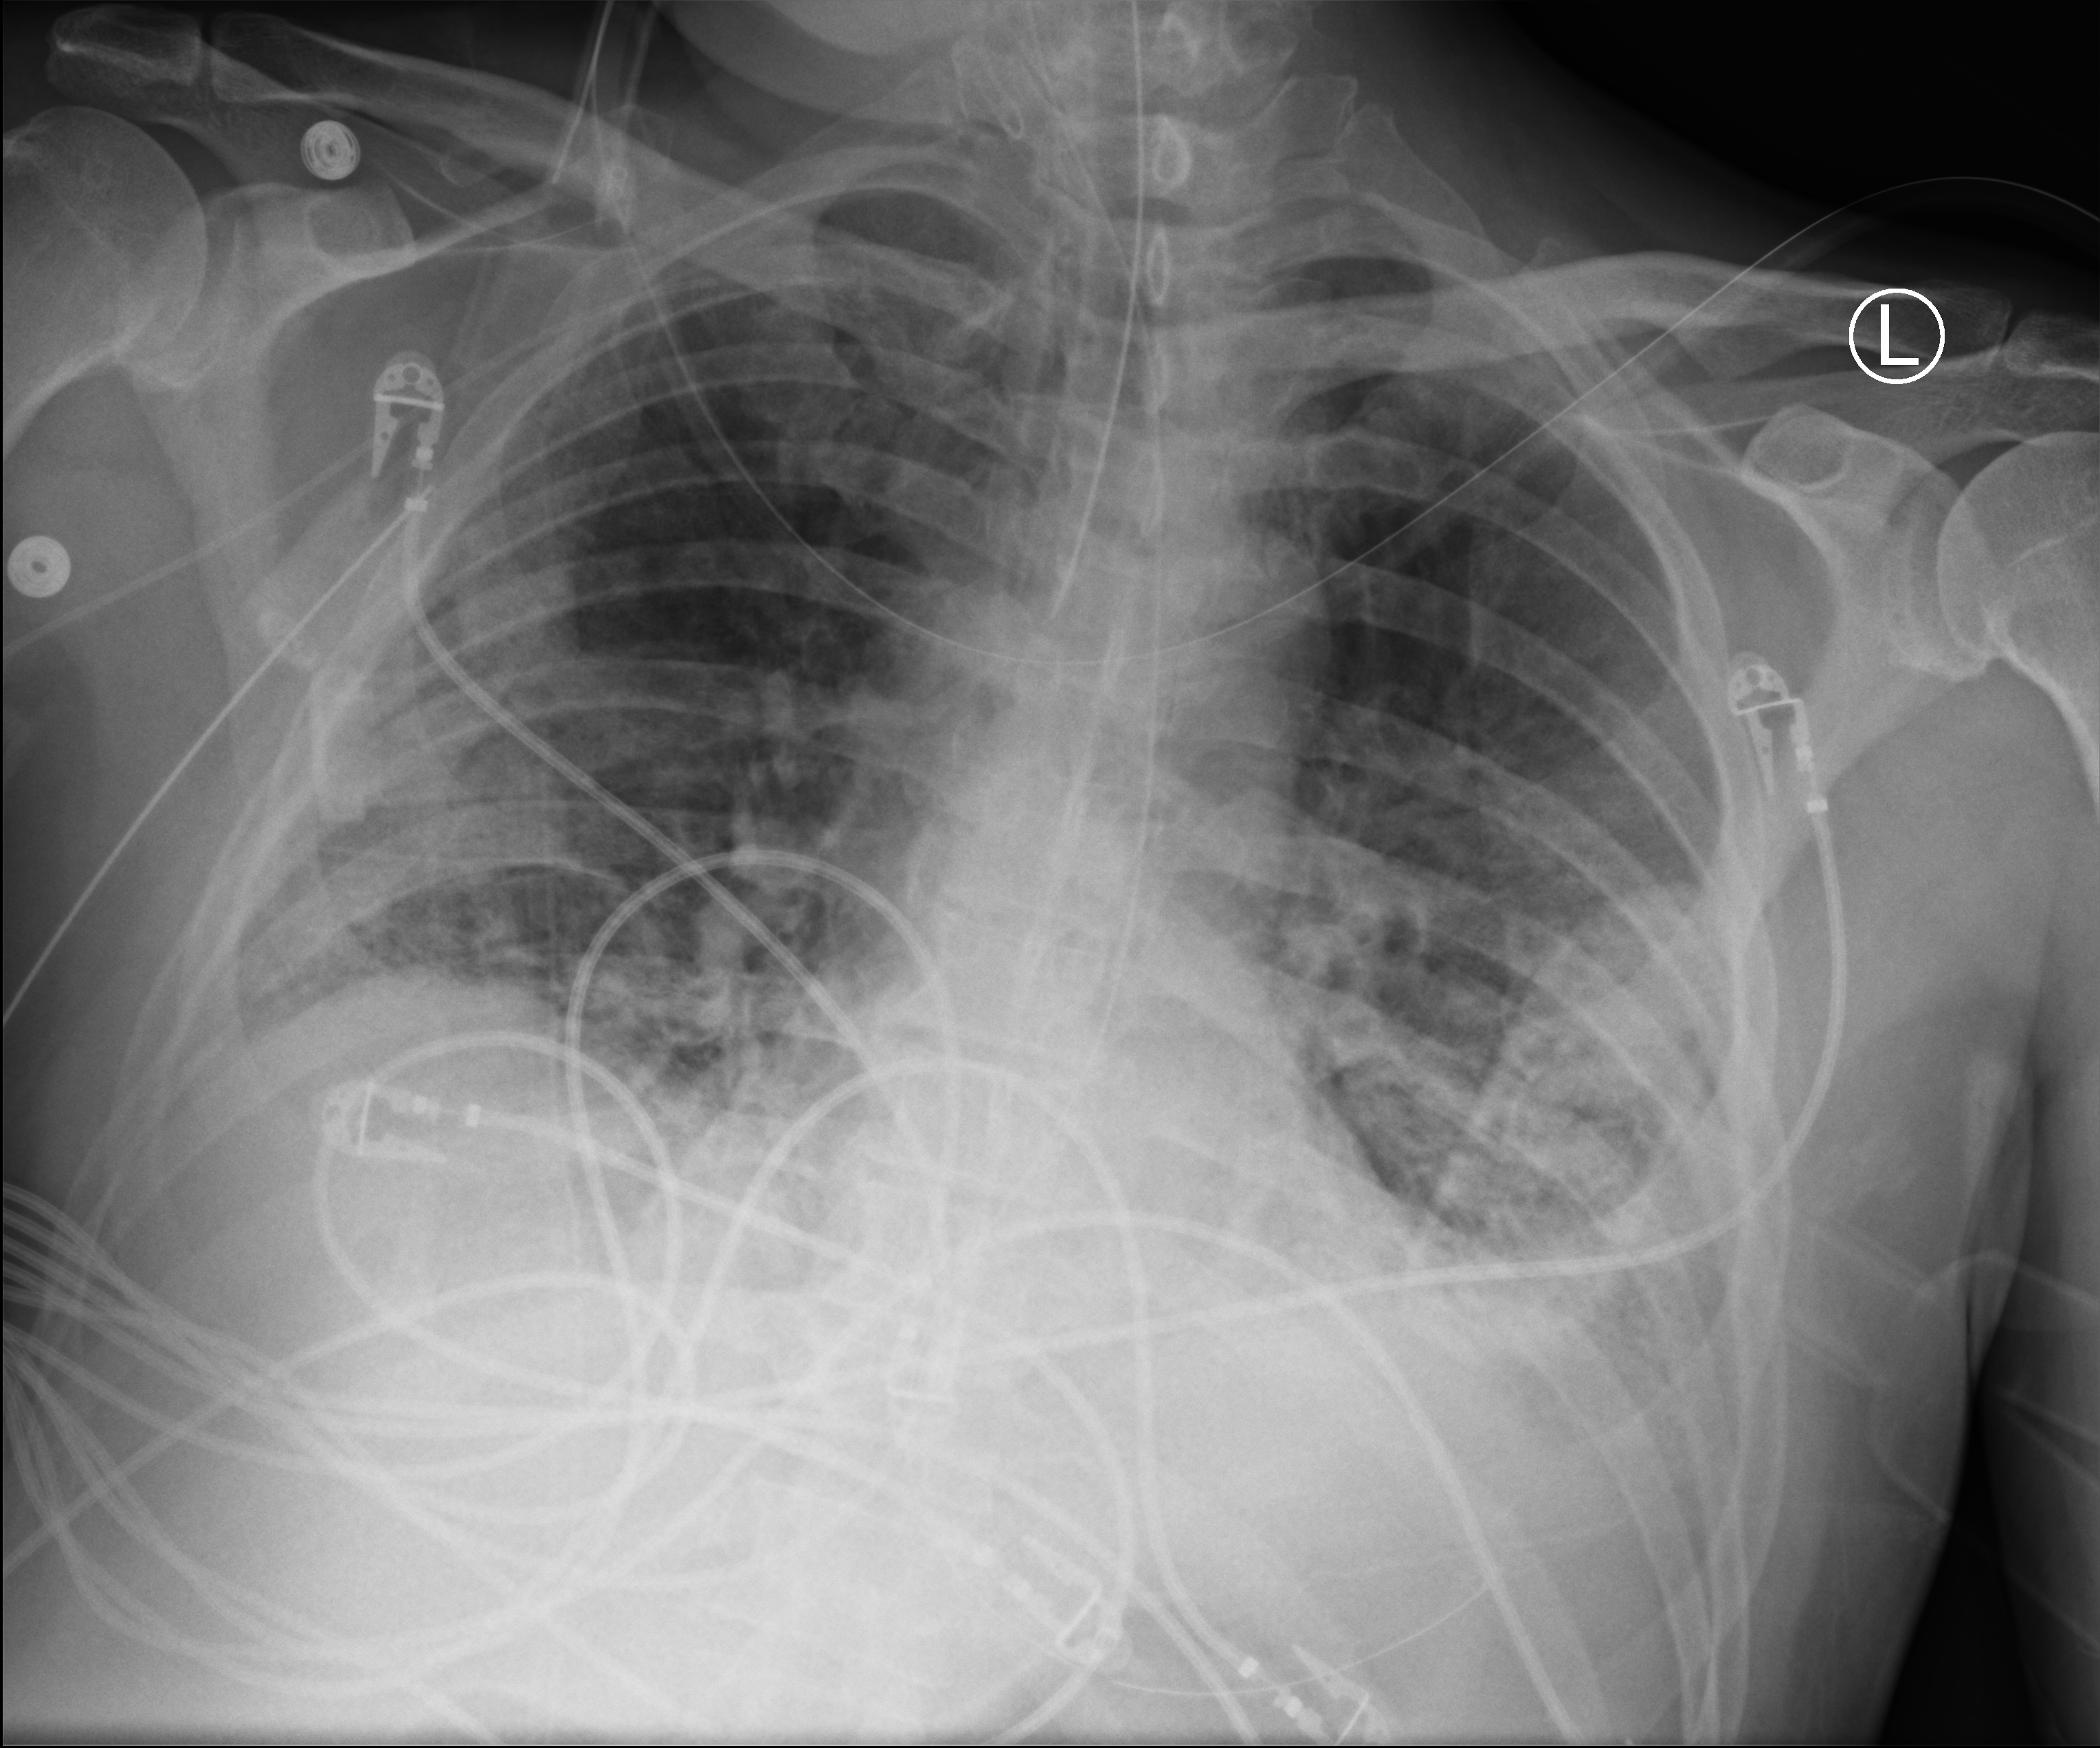
Chest X-ray (portable). Patient hospitalised with COVID-19; male, aged 60–74 years.
Hospital-stay facts (about this admission, not read from this image; timing relative to this image not recorded): admitted to intensive care during this hospital stay: yes; mechanically ventilated during this hospital stay: yes; diabetes (admission record): yes.